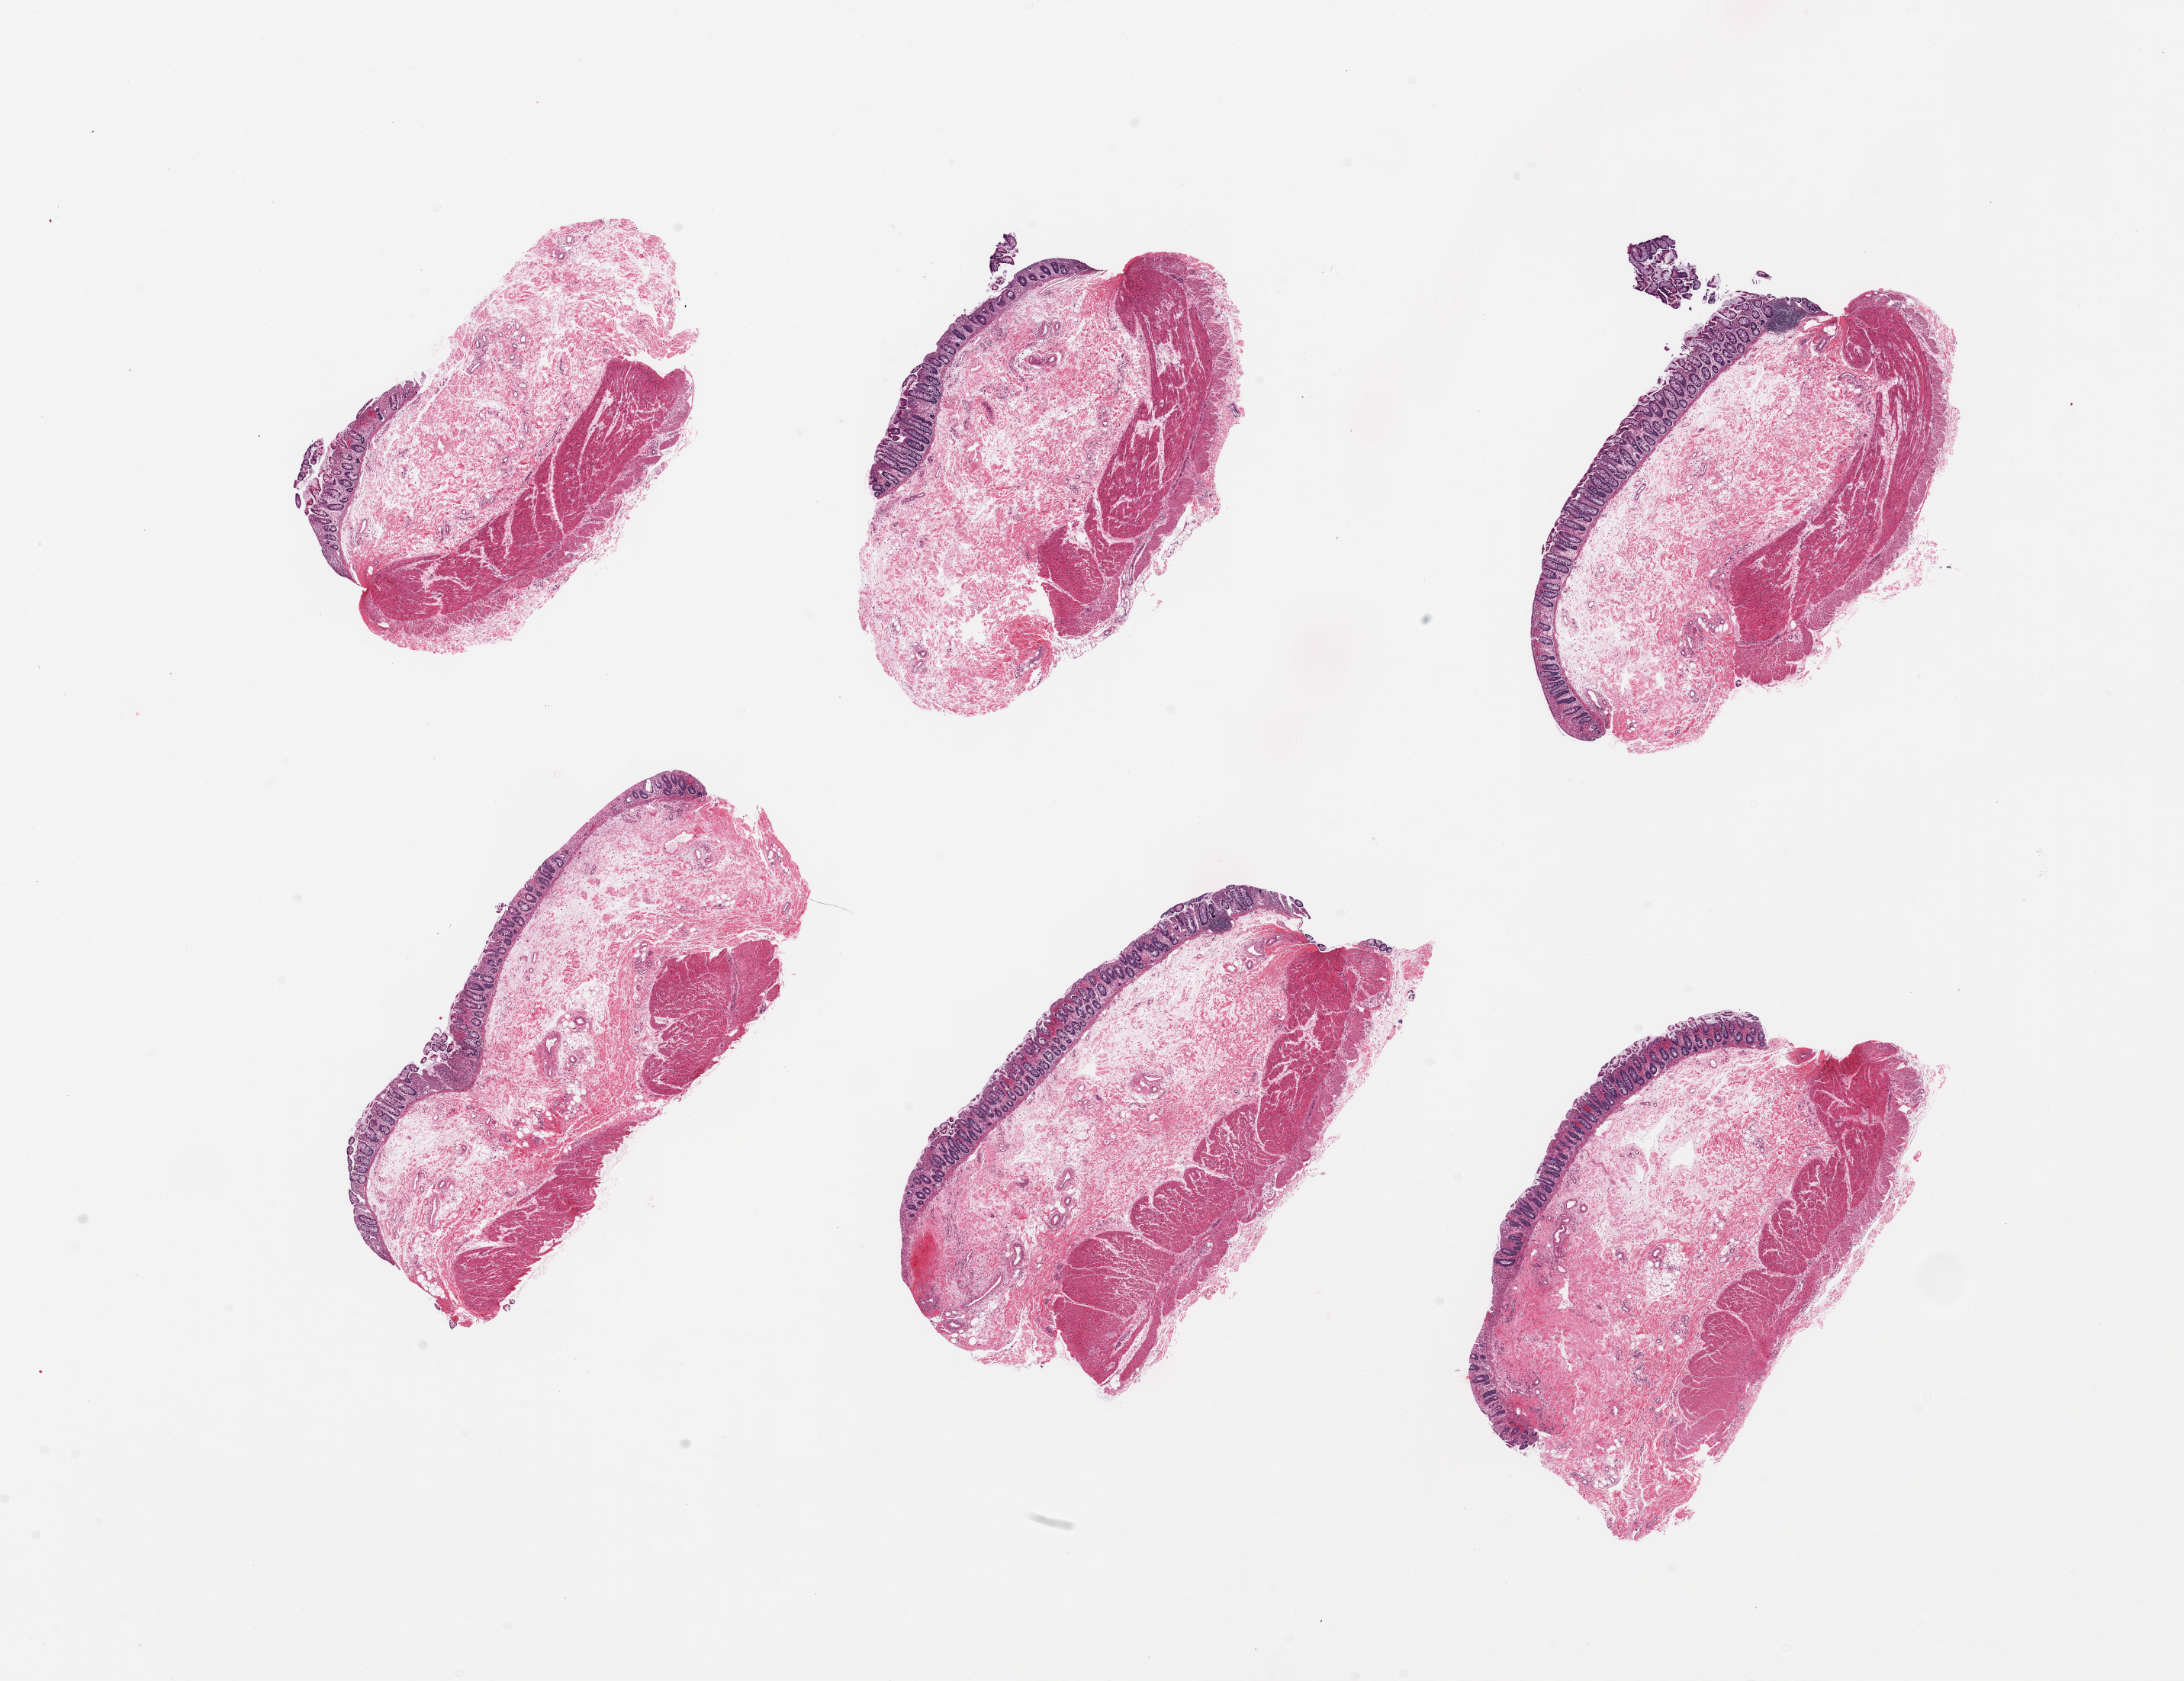
Digitized haematoxylin and eosin-stained section, shown as a low-resolution overview of the whole scanned area (about 22.6 x 17.4 mm, slide scanned at 20x); PAXgene-fixed paraffin-embedded (PFPE) section; target tissue: transverse colon; tissue donor sample.
• pathologist's review note for this sample: 6 pieces, target mucosa is ~0.35mm, 10-15% of thickness